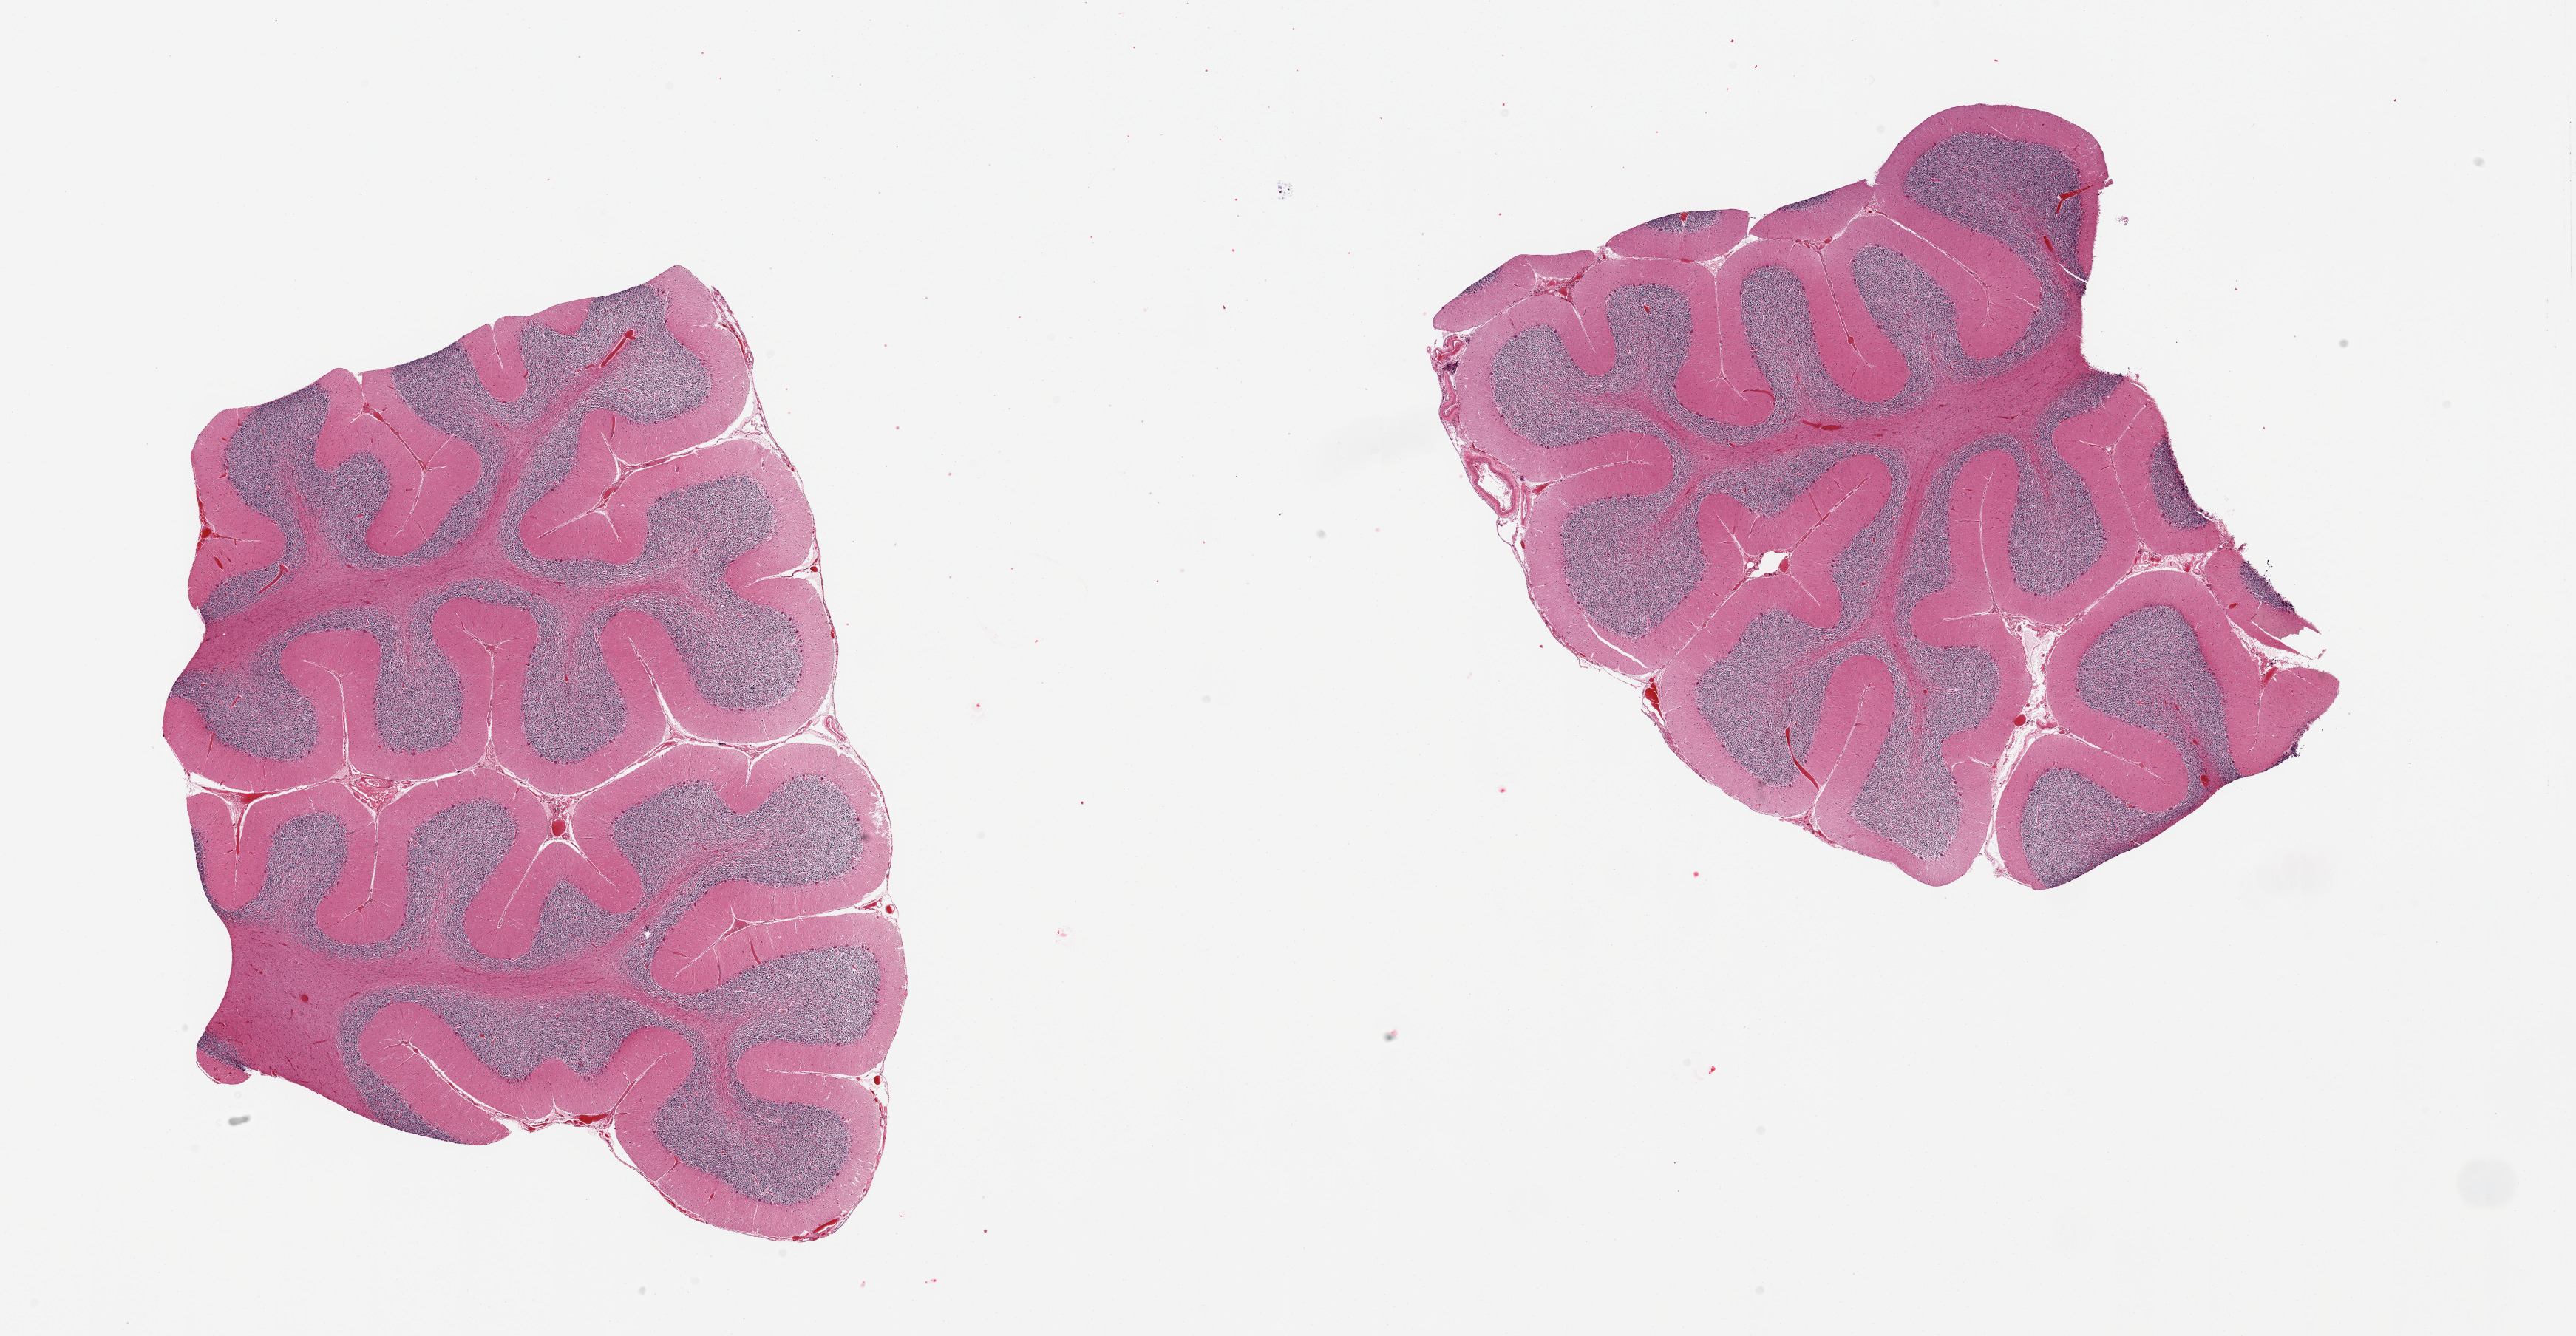
Hematoxylin and eosin (H&E) whole-slide image — shown as a low-resolution overview of the whole scanned area (about 27.6 x 14.3 mm, acquisition: 20x scan); PAXgene-fixed paraffin-embedded (PFPE) section; section of cerebellum (target tissue); tissue donor sample.
Pathologist's review note for this sample: 2 pieces.